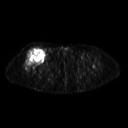
FDG PET of an extremity soft-tissue mass (from a PET/CT study), one axial slice. Position 272 of 311 along the scan axis. 3.27 mm slice thickness. 128 × 128 image matrix, field of view 500 × 500 mm. Female patient, age 57 years. From the clinical record (not read from this slice): histological type: pleiomorphic undifferentiated sarcoma; grade: high; site of the primary tumour: right quadricep.
Outlined on this slice (expert contour drawn on MRI and transferred to this co-registered scan by the dataset authors):
- tumour plus oedema (research contour): bounding box <24,47,44,68> (left, top, right, bottom; pixels)
- tumour (research contour): <24,47,44,68>